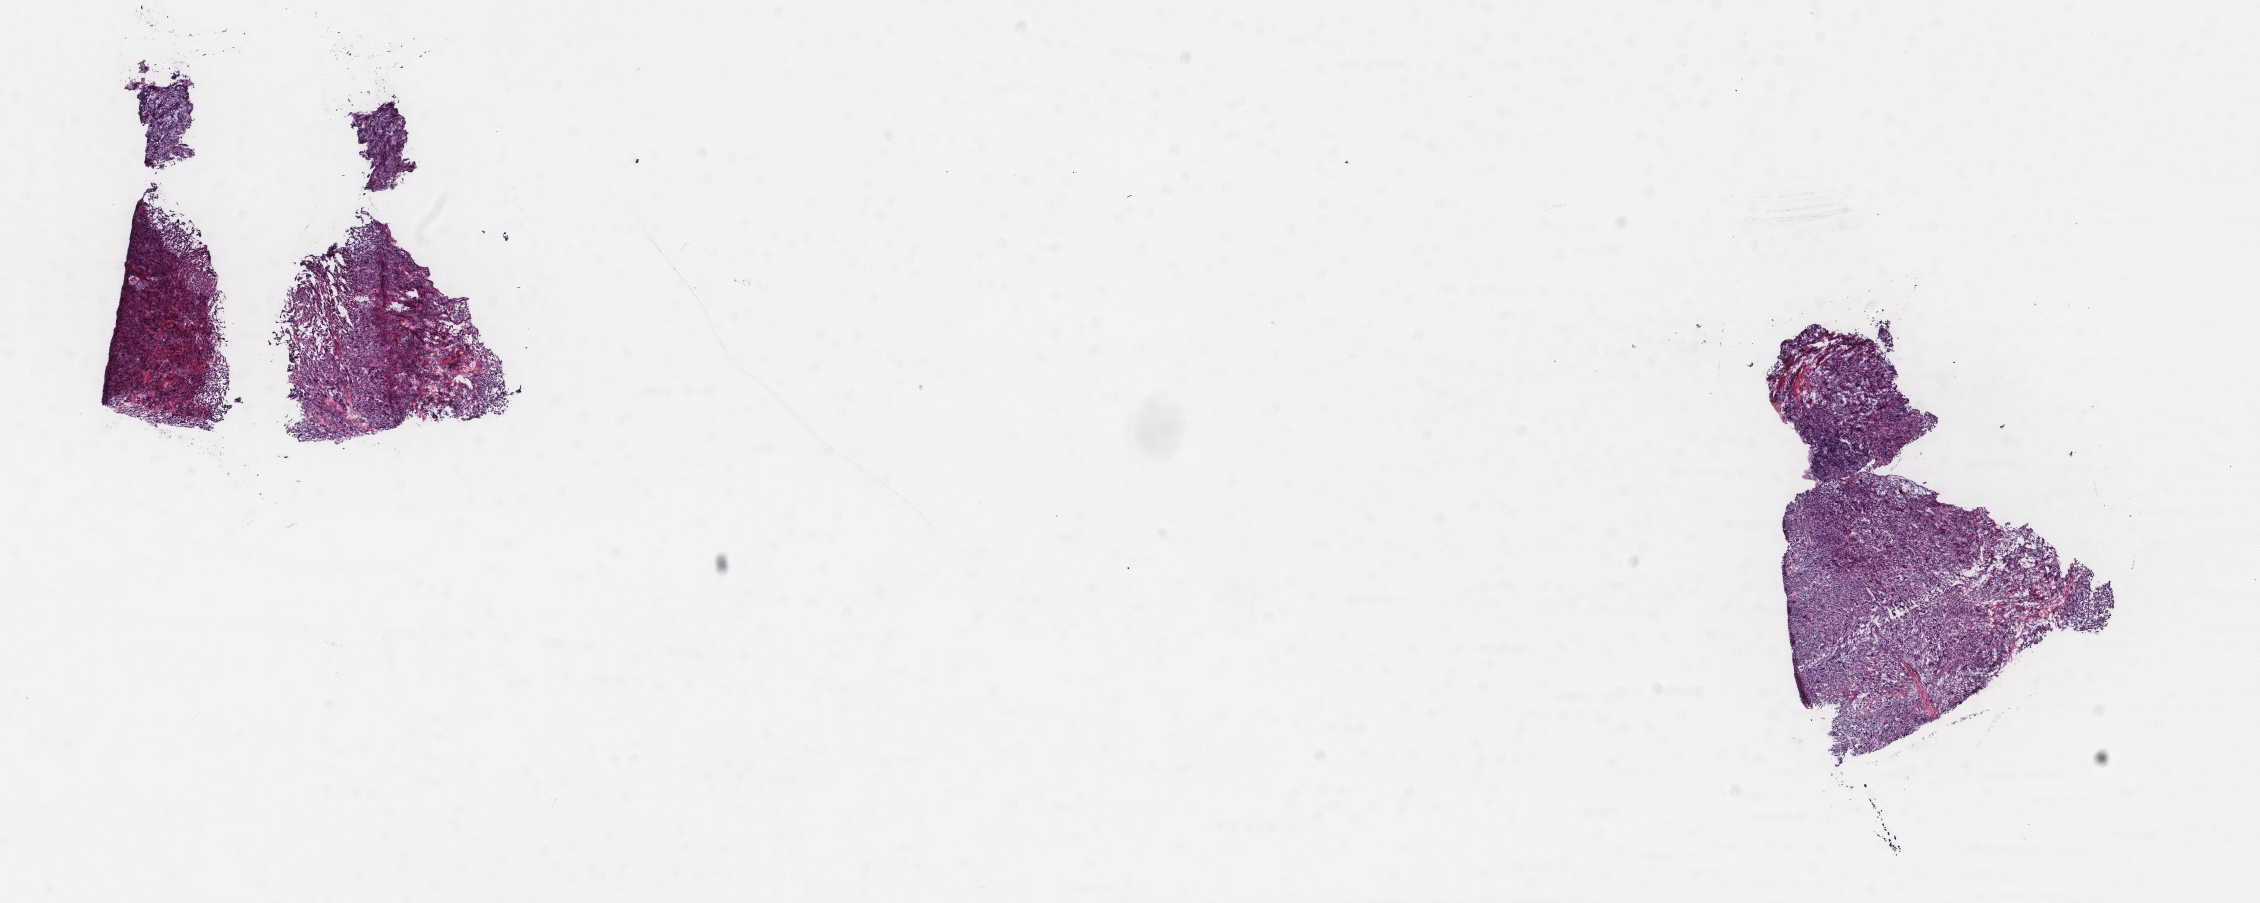
H&E whole-slide image, whole scanned area (about 17.9 x 7.2 mm, acquisition: 40x scan) shown as a low-resolution overview; frozen section from the top of the tissue portion; metastatic tumour sample, sampled site: connective, subcutaneous and other soft tissues of trunk. Male patient; age at initial diagnosis 79 years.
This section: metastatic tumour tissue. Patient diagnosis: Malignant melanoma, NOS.